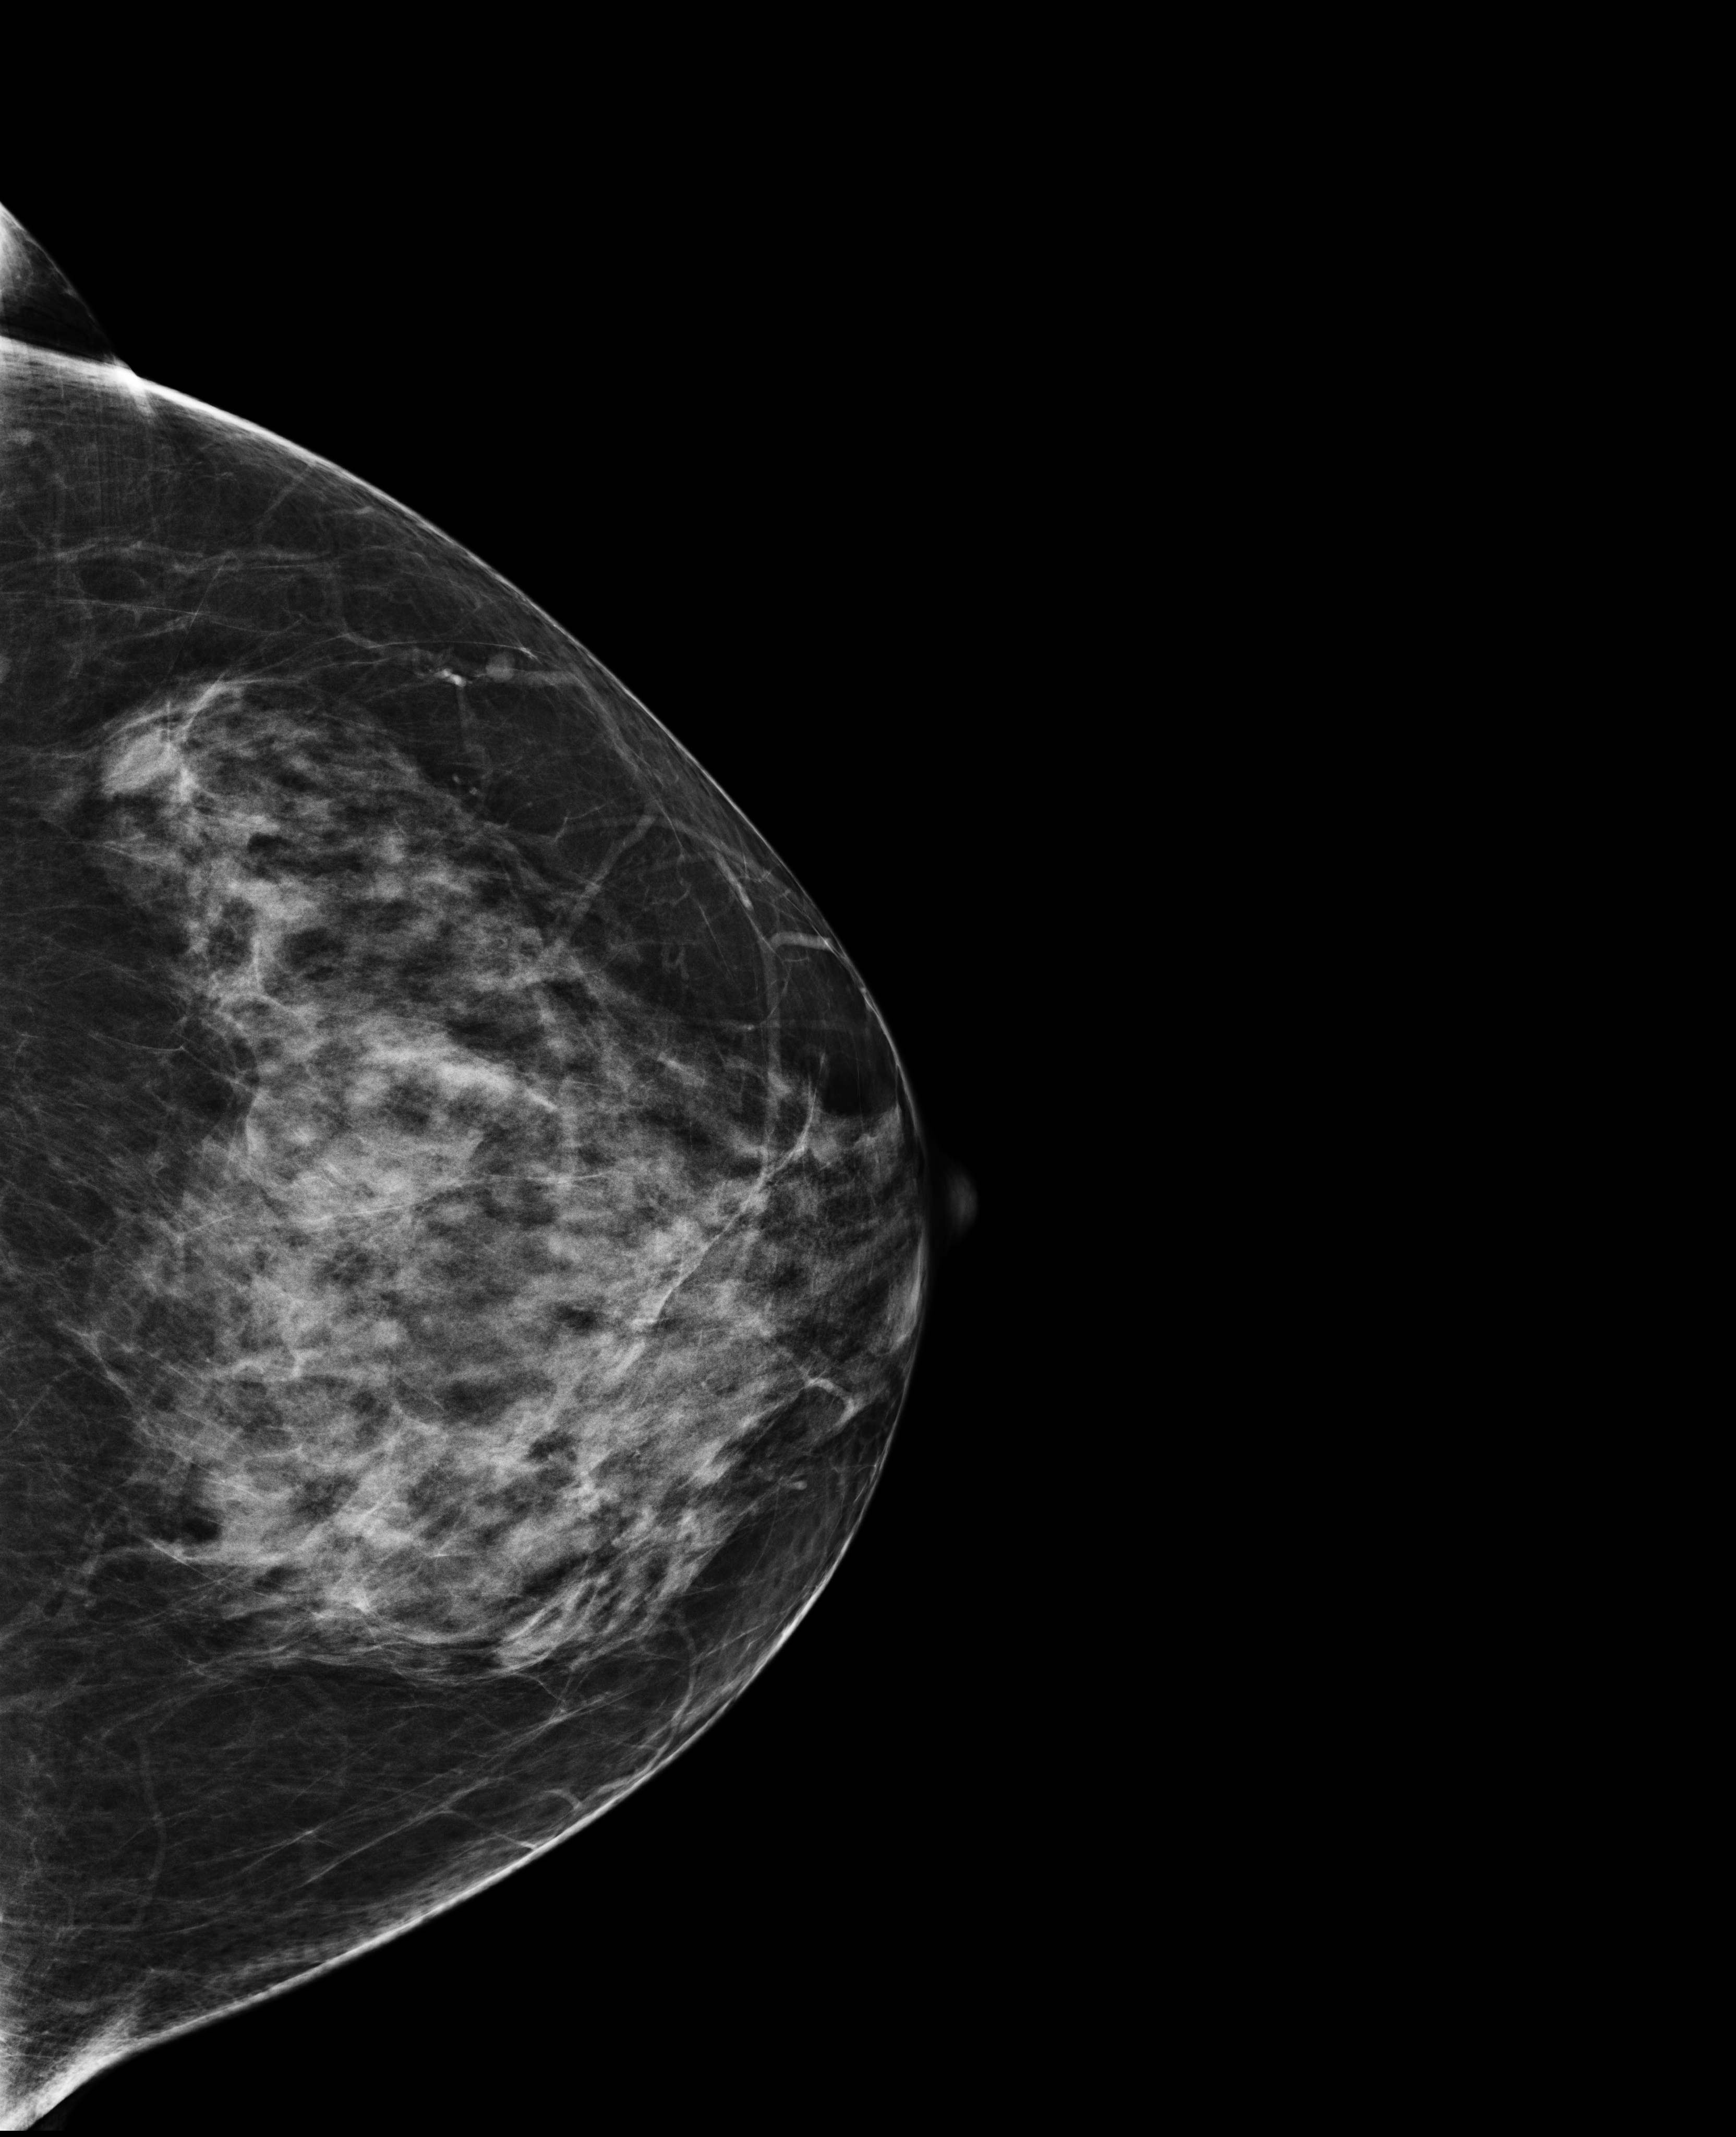
Full-field digital mammogram (FFDM); left breast; cranio-caudal projection; screening examination; compressed breast thickness 72 mm; system: Selenia Dimensions. Patient aged 59 years (female).
BI-RADS breast density category at the screening exam (both breasts, scale 1–4): 3. Final BI-RADS assessment for this screening round (tomosynthesis exam, both breasts): category 2. Recall: no recall after this screen.